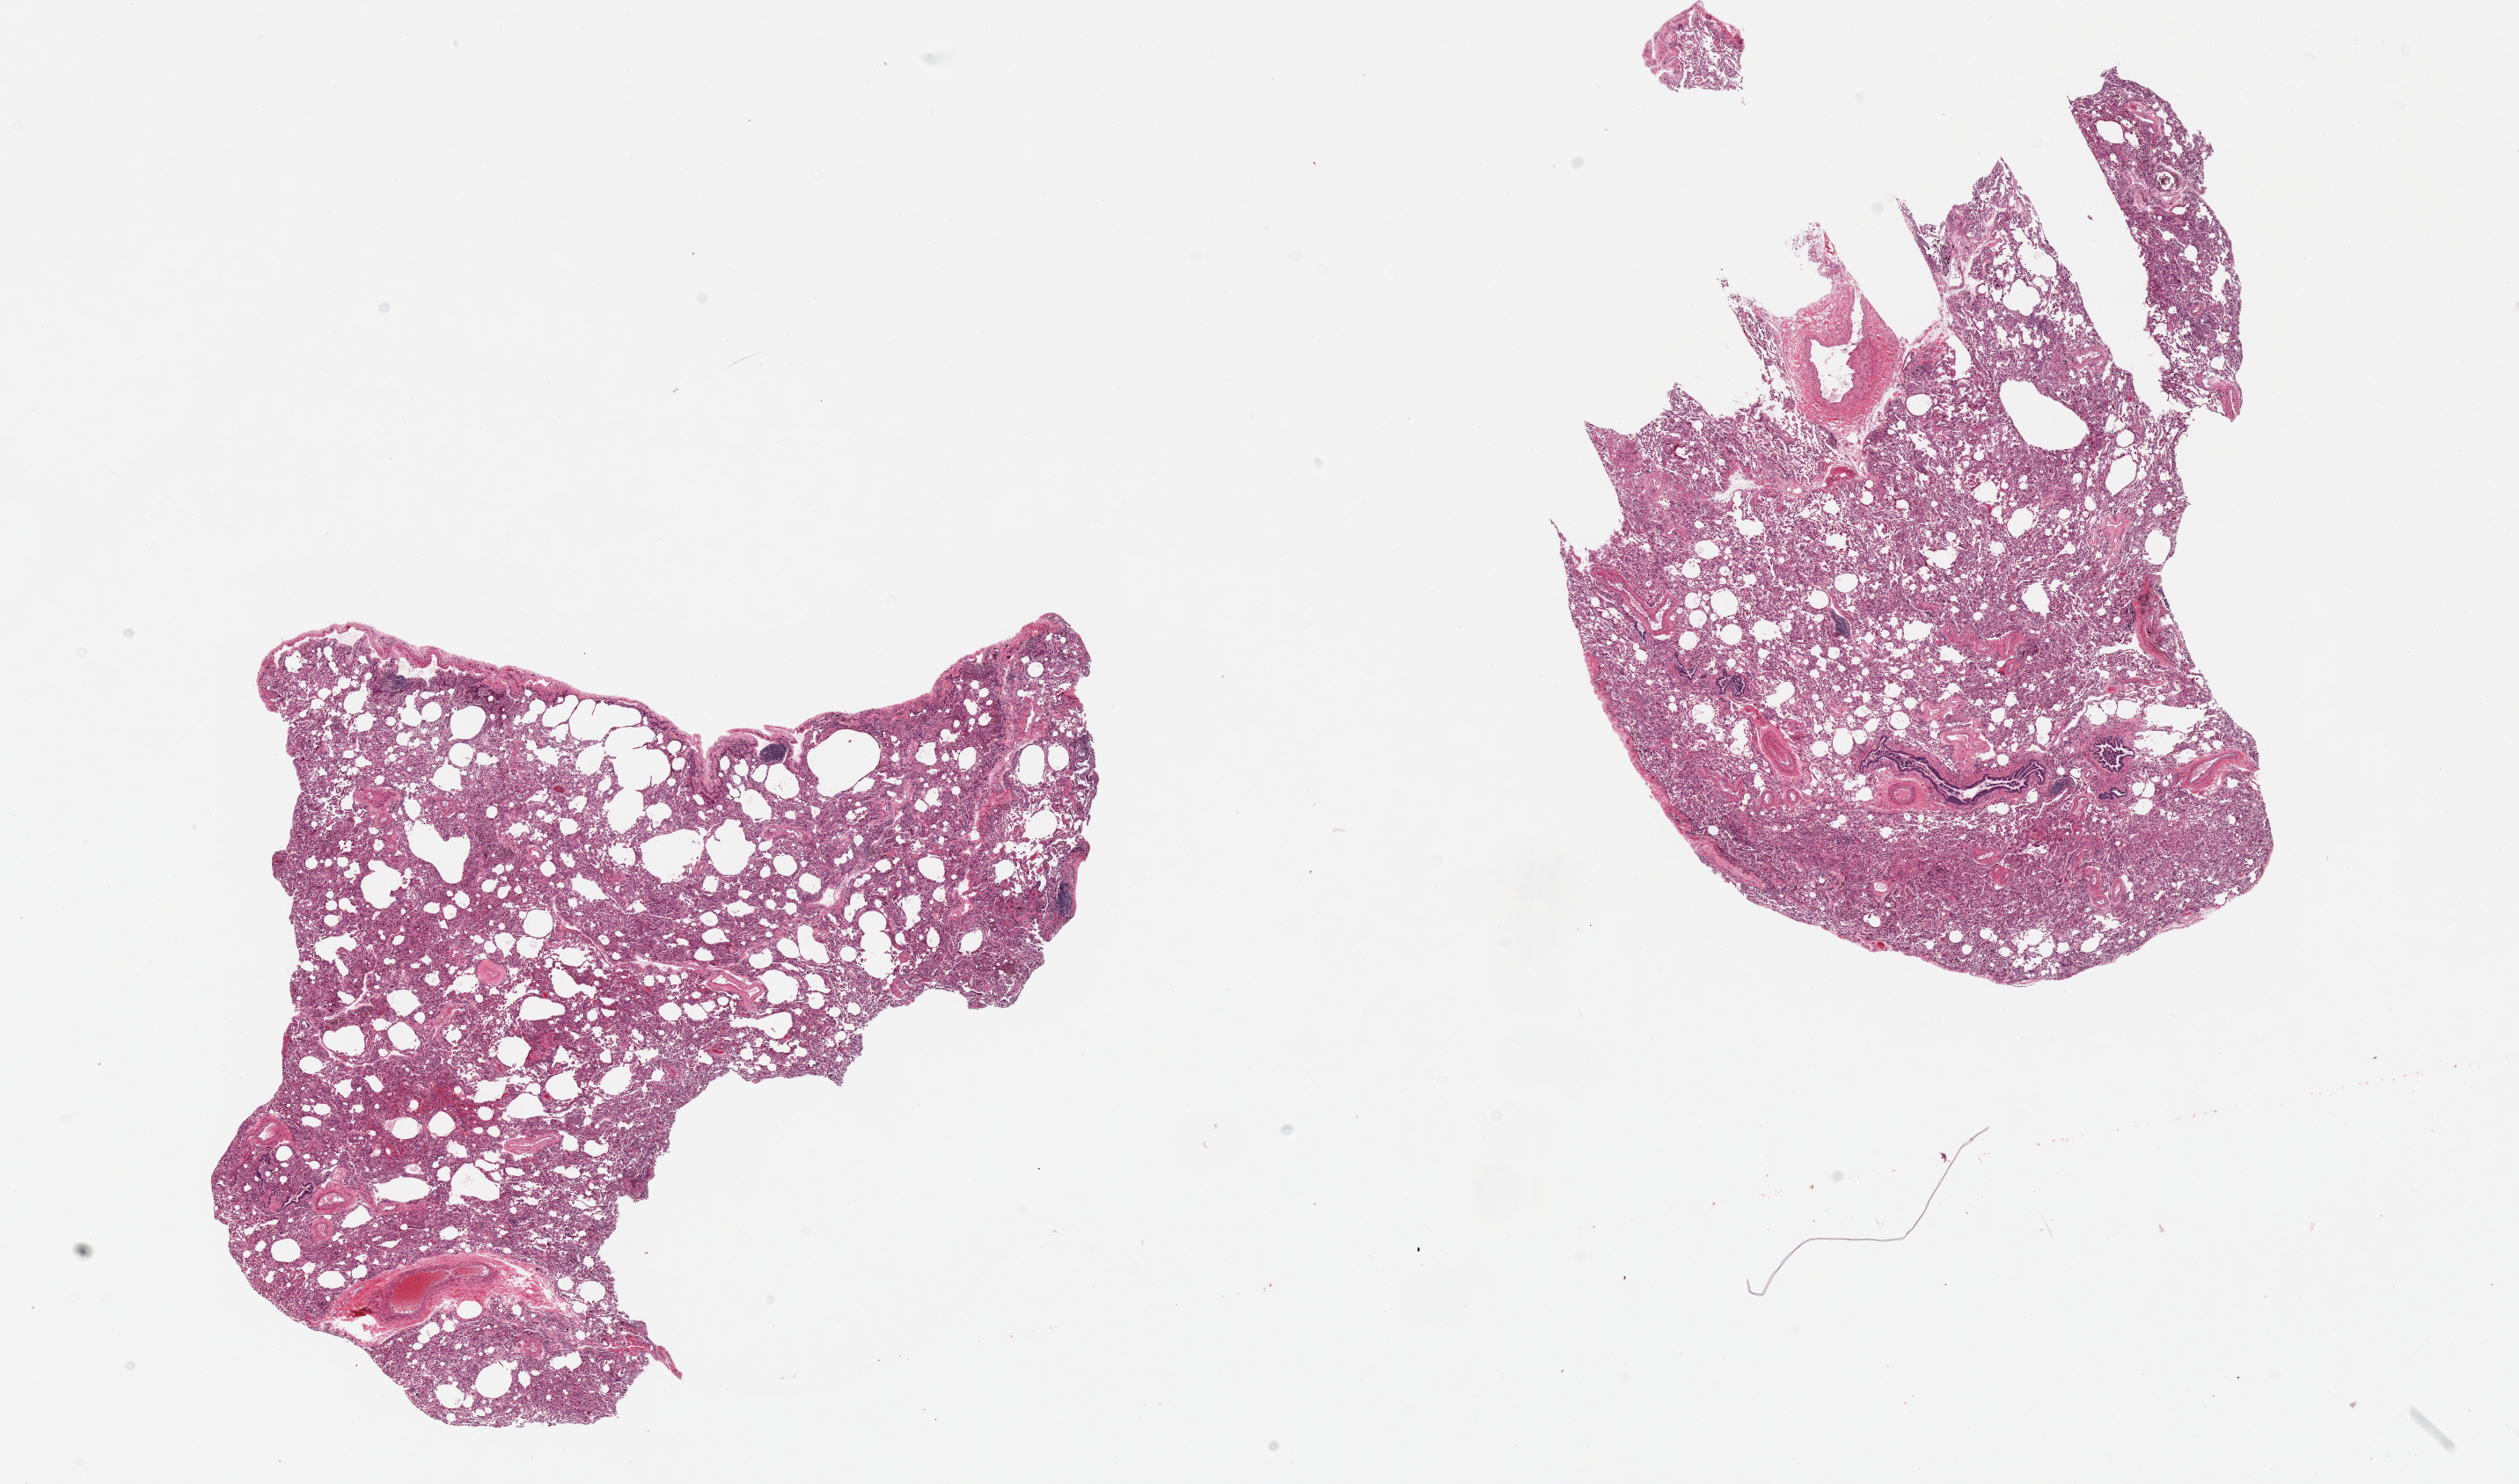
Whole-slide image, haematoxylin and eosin stain — whole scanned area (about 22.6 x 13.3 mm, acquisition: 20x scan) shown as a low-resolution overview, PAXgene-fixed, paraffin-embedded tissue, sampled site (target tissue): lung, tissue donor sample. Donor sex: male.
Pathologist's review note for this sample: 2 pieces, atelectasis, numerous hemosiderin-laden macrophages and focal hemorrhage.